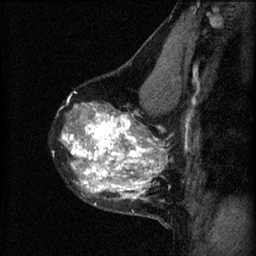
Breast MRI (dynamic contrast-enhanced), one sagittal slice. Position 40 of 60 along the scan axis. 3 images stored at this slice position (order not interpretable as contrast timing). 1.5 T. TE 4.2 ms, TR 8.2 ms. 2 mm slice thickness. 256 × 256 image matrix, field of view 180 × 180 mm. Patient: female, 40 years.
Annotated regions visible in this slice (semi-automatically segmented with operator editing):
- analysis volume of interest (the breast-tissue region the enhancement analysis was run in; not a lesion): bounding box [x1, y1, x2, y2] px = [60, 76, 179, 219]
- tumour enhancement mask (voxels above the 70 % enhancement threshold inside the analysis volume of interest): [62, 104, 163, 201]